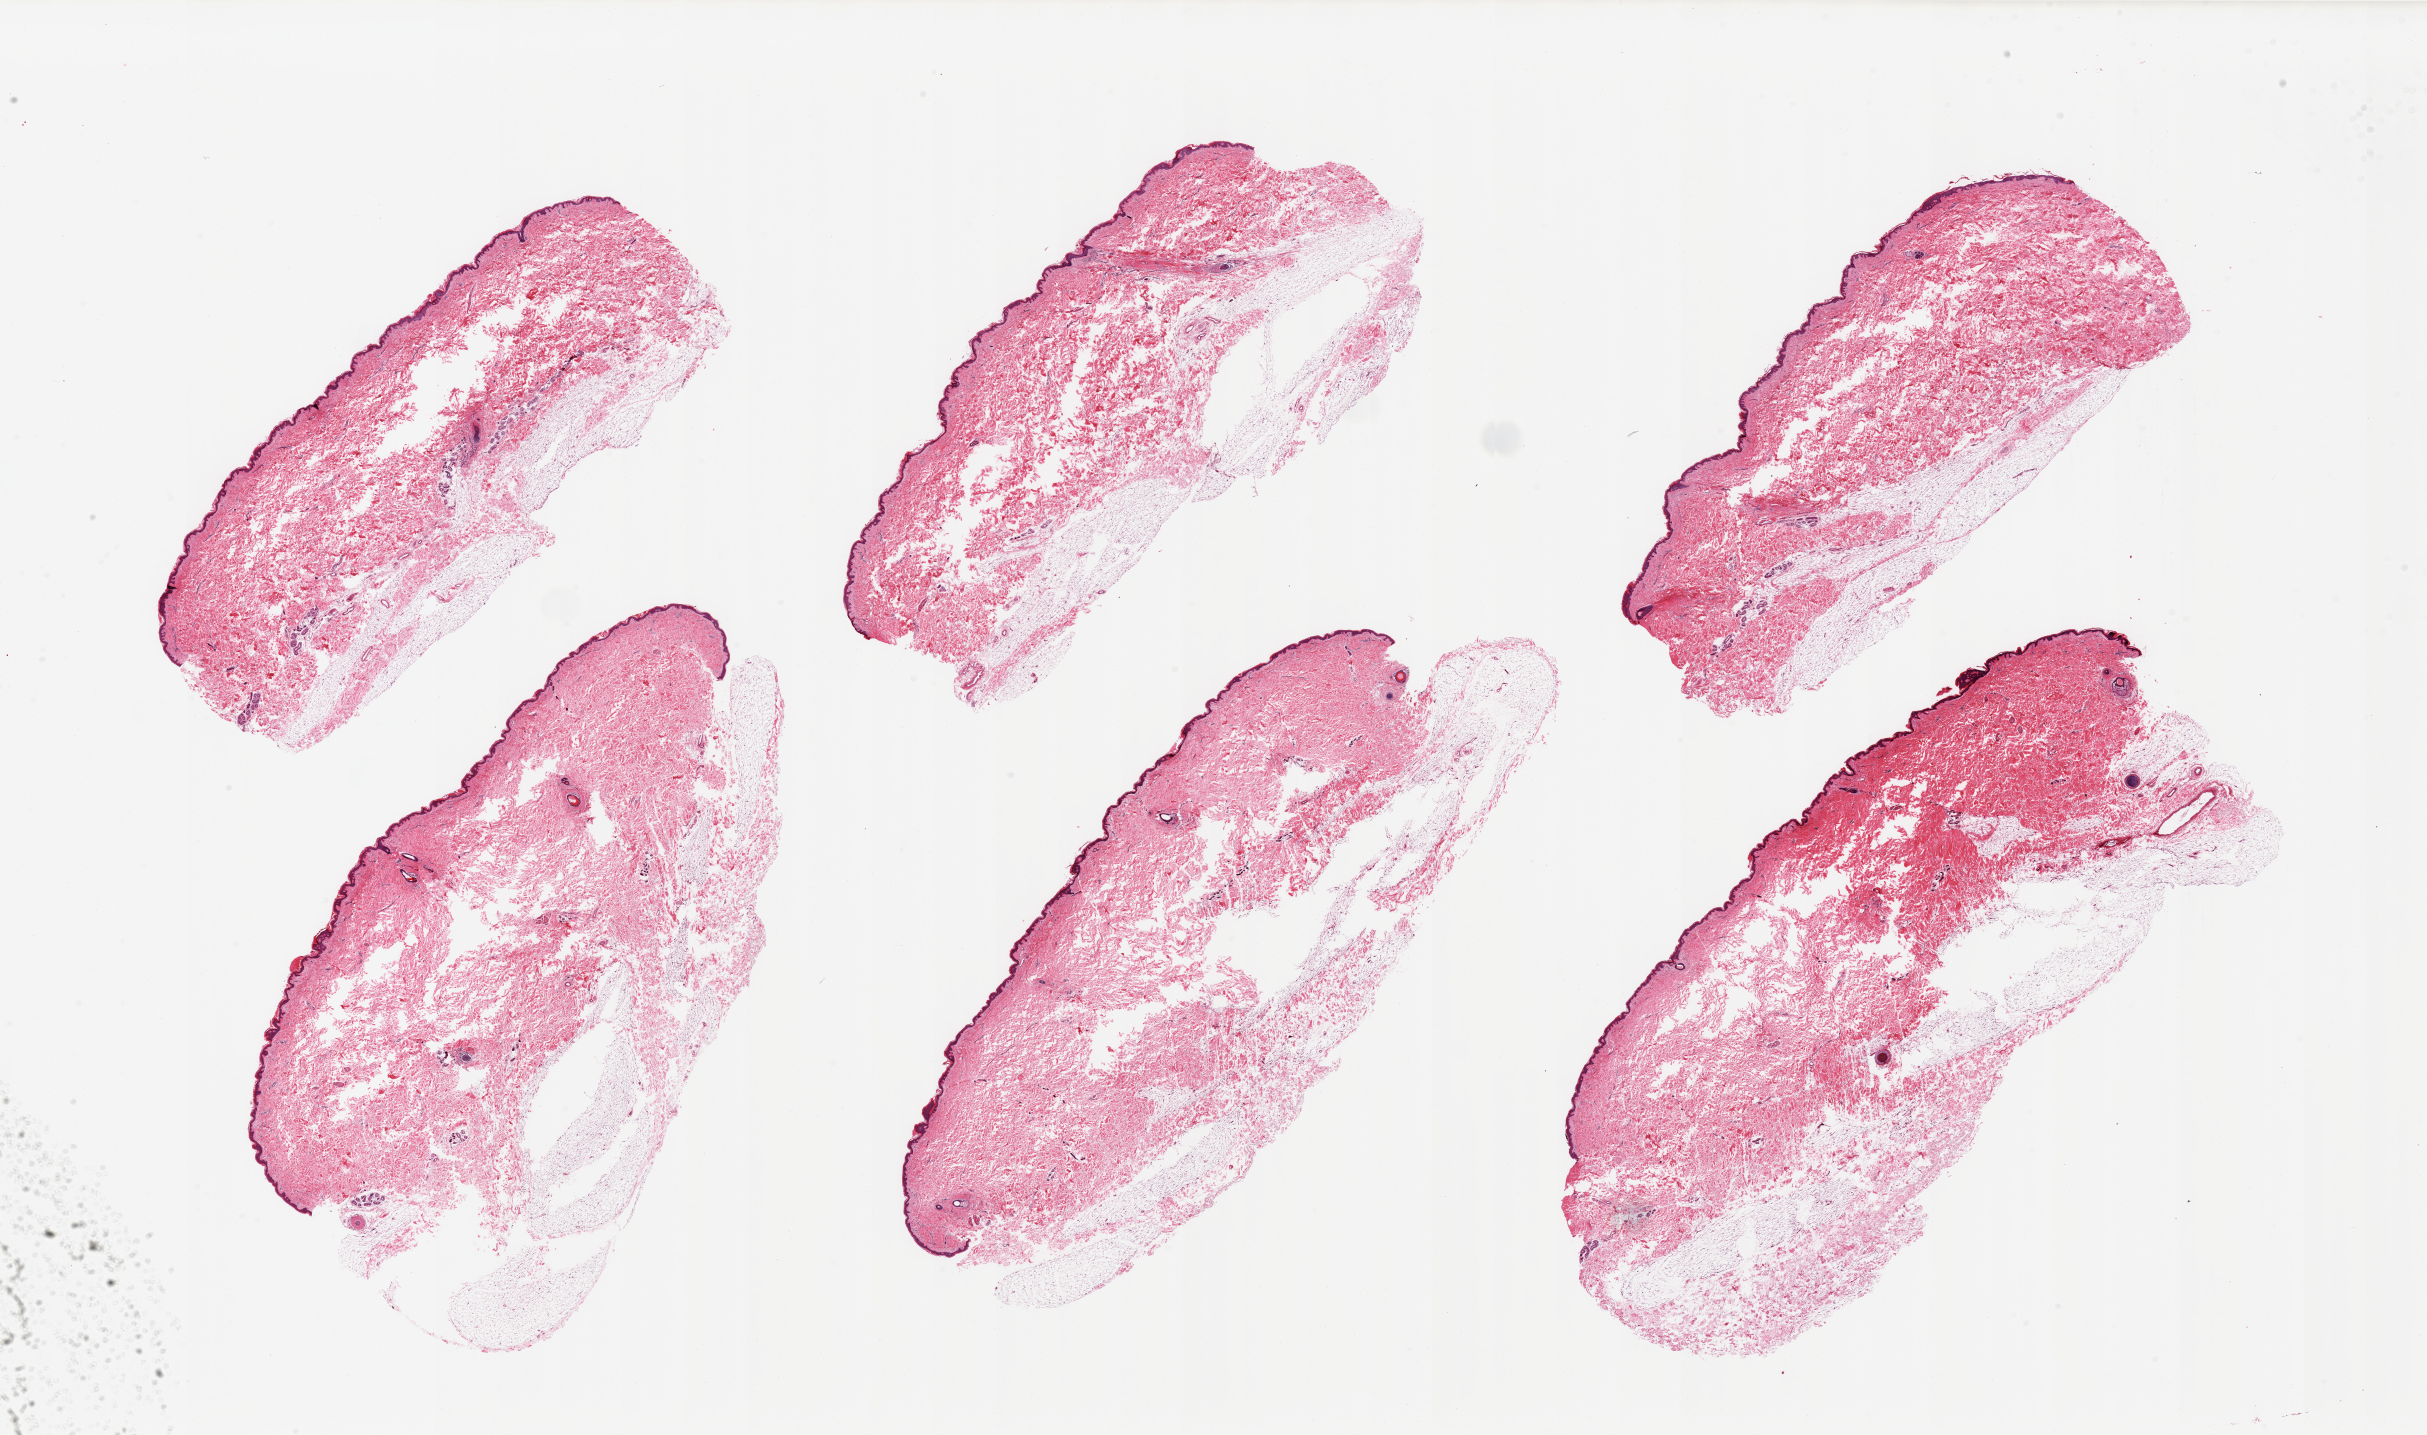
H&E whole-slide image, low-resolution overview of the scanned area, about 38.4 x 22.7 mm; PAXgene-fixed, paraffin-embedded tissue; section of skin of suprapubic region (target tissue); donor tissue sample. Female donor.
Pathologist's review note for this sample: 6 pieces, adherent dermal fat up to ~2mm; squamous epithelium is ~40-50 microns.